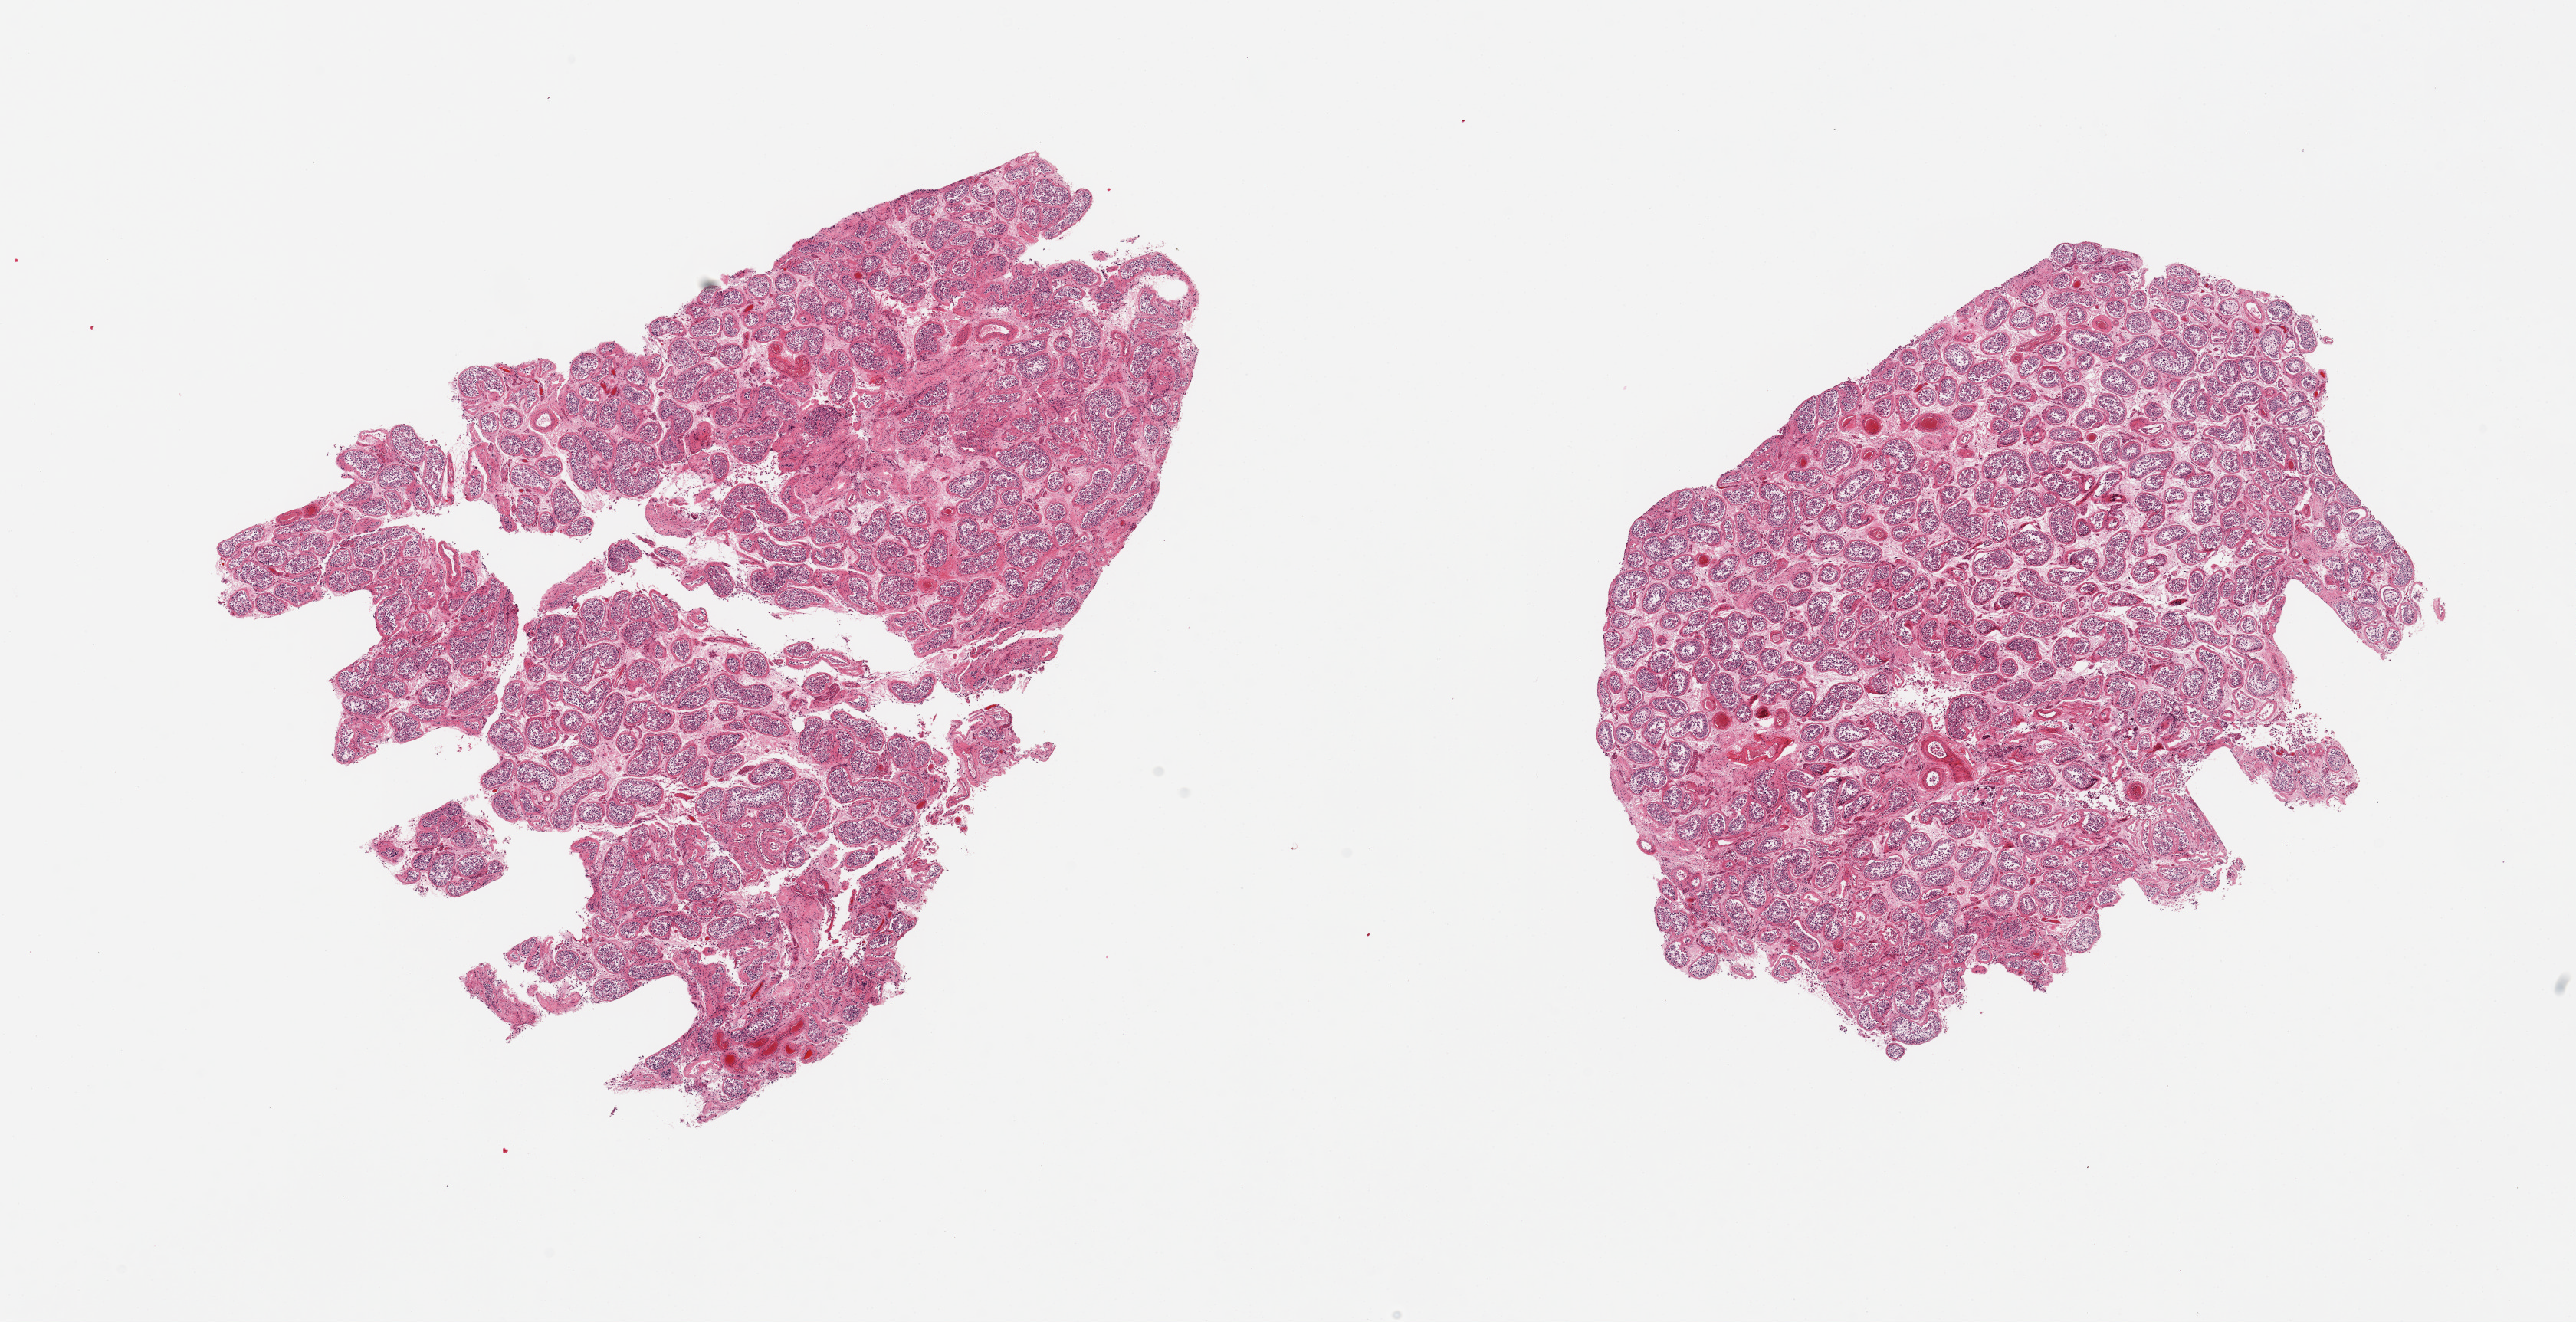
Digitized haematoxylin and eosin-stained section — low-resolution overview of the scanned area, about 26.6 x 13.6 mm (from a 20x scan). PAXgene-fixed paraffin-embedded (PFPE) section. Sampled site (target tissue): testis. Tissue donor sample. Donor: male.
* review note (as recorded): 2 pieces; increased peritubular fibrosis and some hyalinized tubules